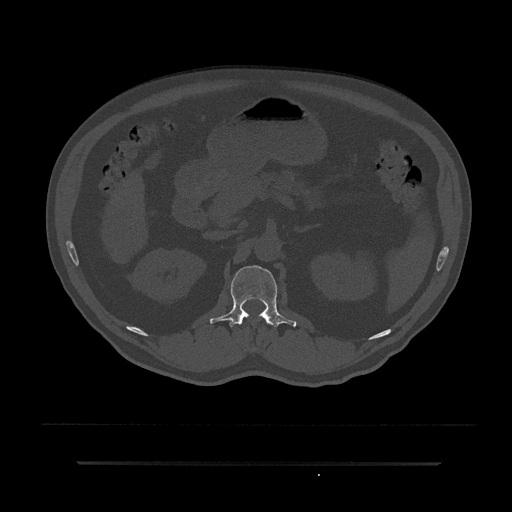
CT including the spine, one axial slice; slice 154 of 797 in the series (ordered by position); reconstruction kernel Br40s/3; 120 kVp; bone window (W 1800 / L 400 HU); 0.5 mm slice thickness; 512 × 512 image matrix, field of view 464 × 464 mm. Male patient, age 59 years. From the clinical record (not read from this slice): primary cancer: bile ducts; vertebrae with lytic lesions (as recorded): T10.
Structures marked on this image (semi-automatic segmentation, software-assisted and operator-edited):
- L1 vertebra: box from (x=210, y=265) to (x=297, y=327) px